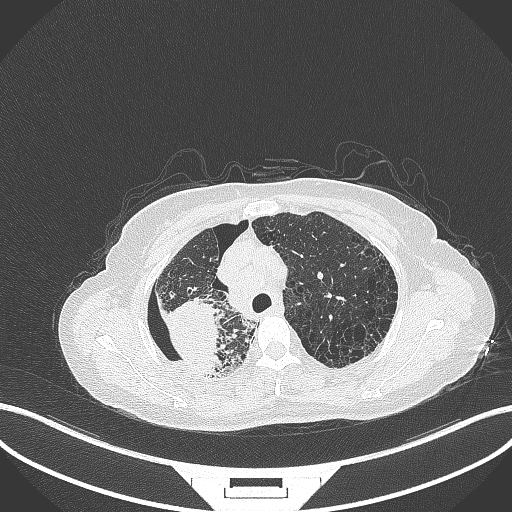
Chest CT, one axial slice; slice 270 of 408 in the series (ordered by position); 120 kVp; lung window (W 1500 / L -600 HU); 1 mm slice thickness; 512 × 512 image matrix, field of view 400 × 400 mm. Patient: female, 64 years. From the clinical record (not read from this slice): clinical TNM (as recorded): T3 N3 M0.
Structures marked on this image (bounding box drawn by a radiologist):
- lung tumour (recorded histology: squamous cell carcinoma): box from (x=159, y=296) to (x=222, y=382) px